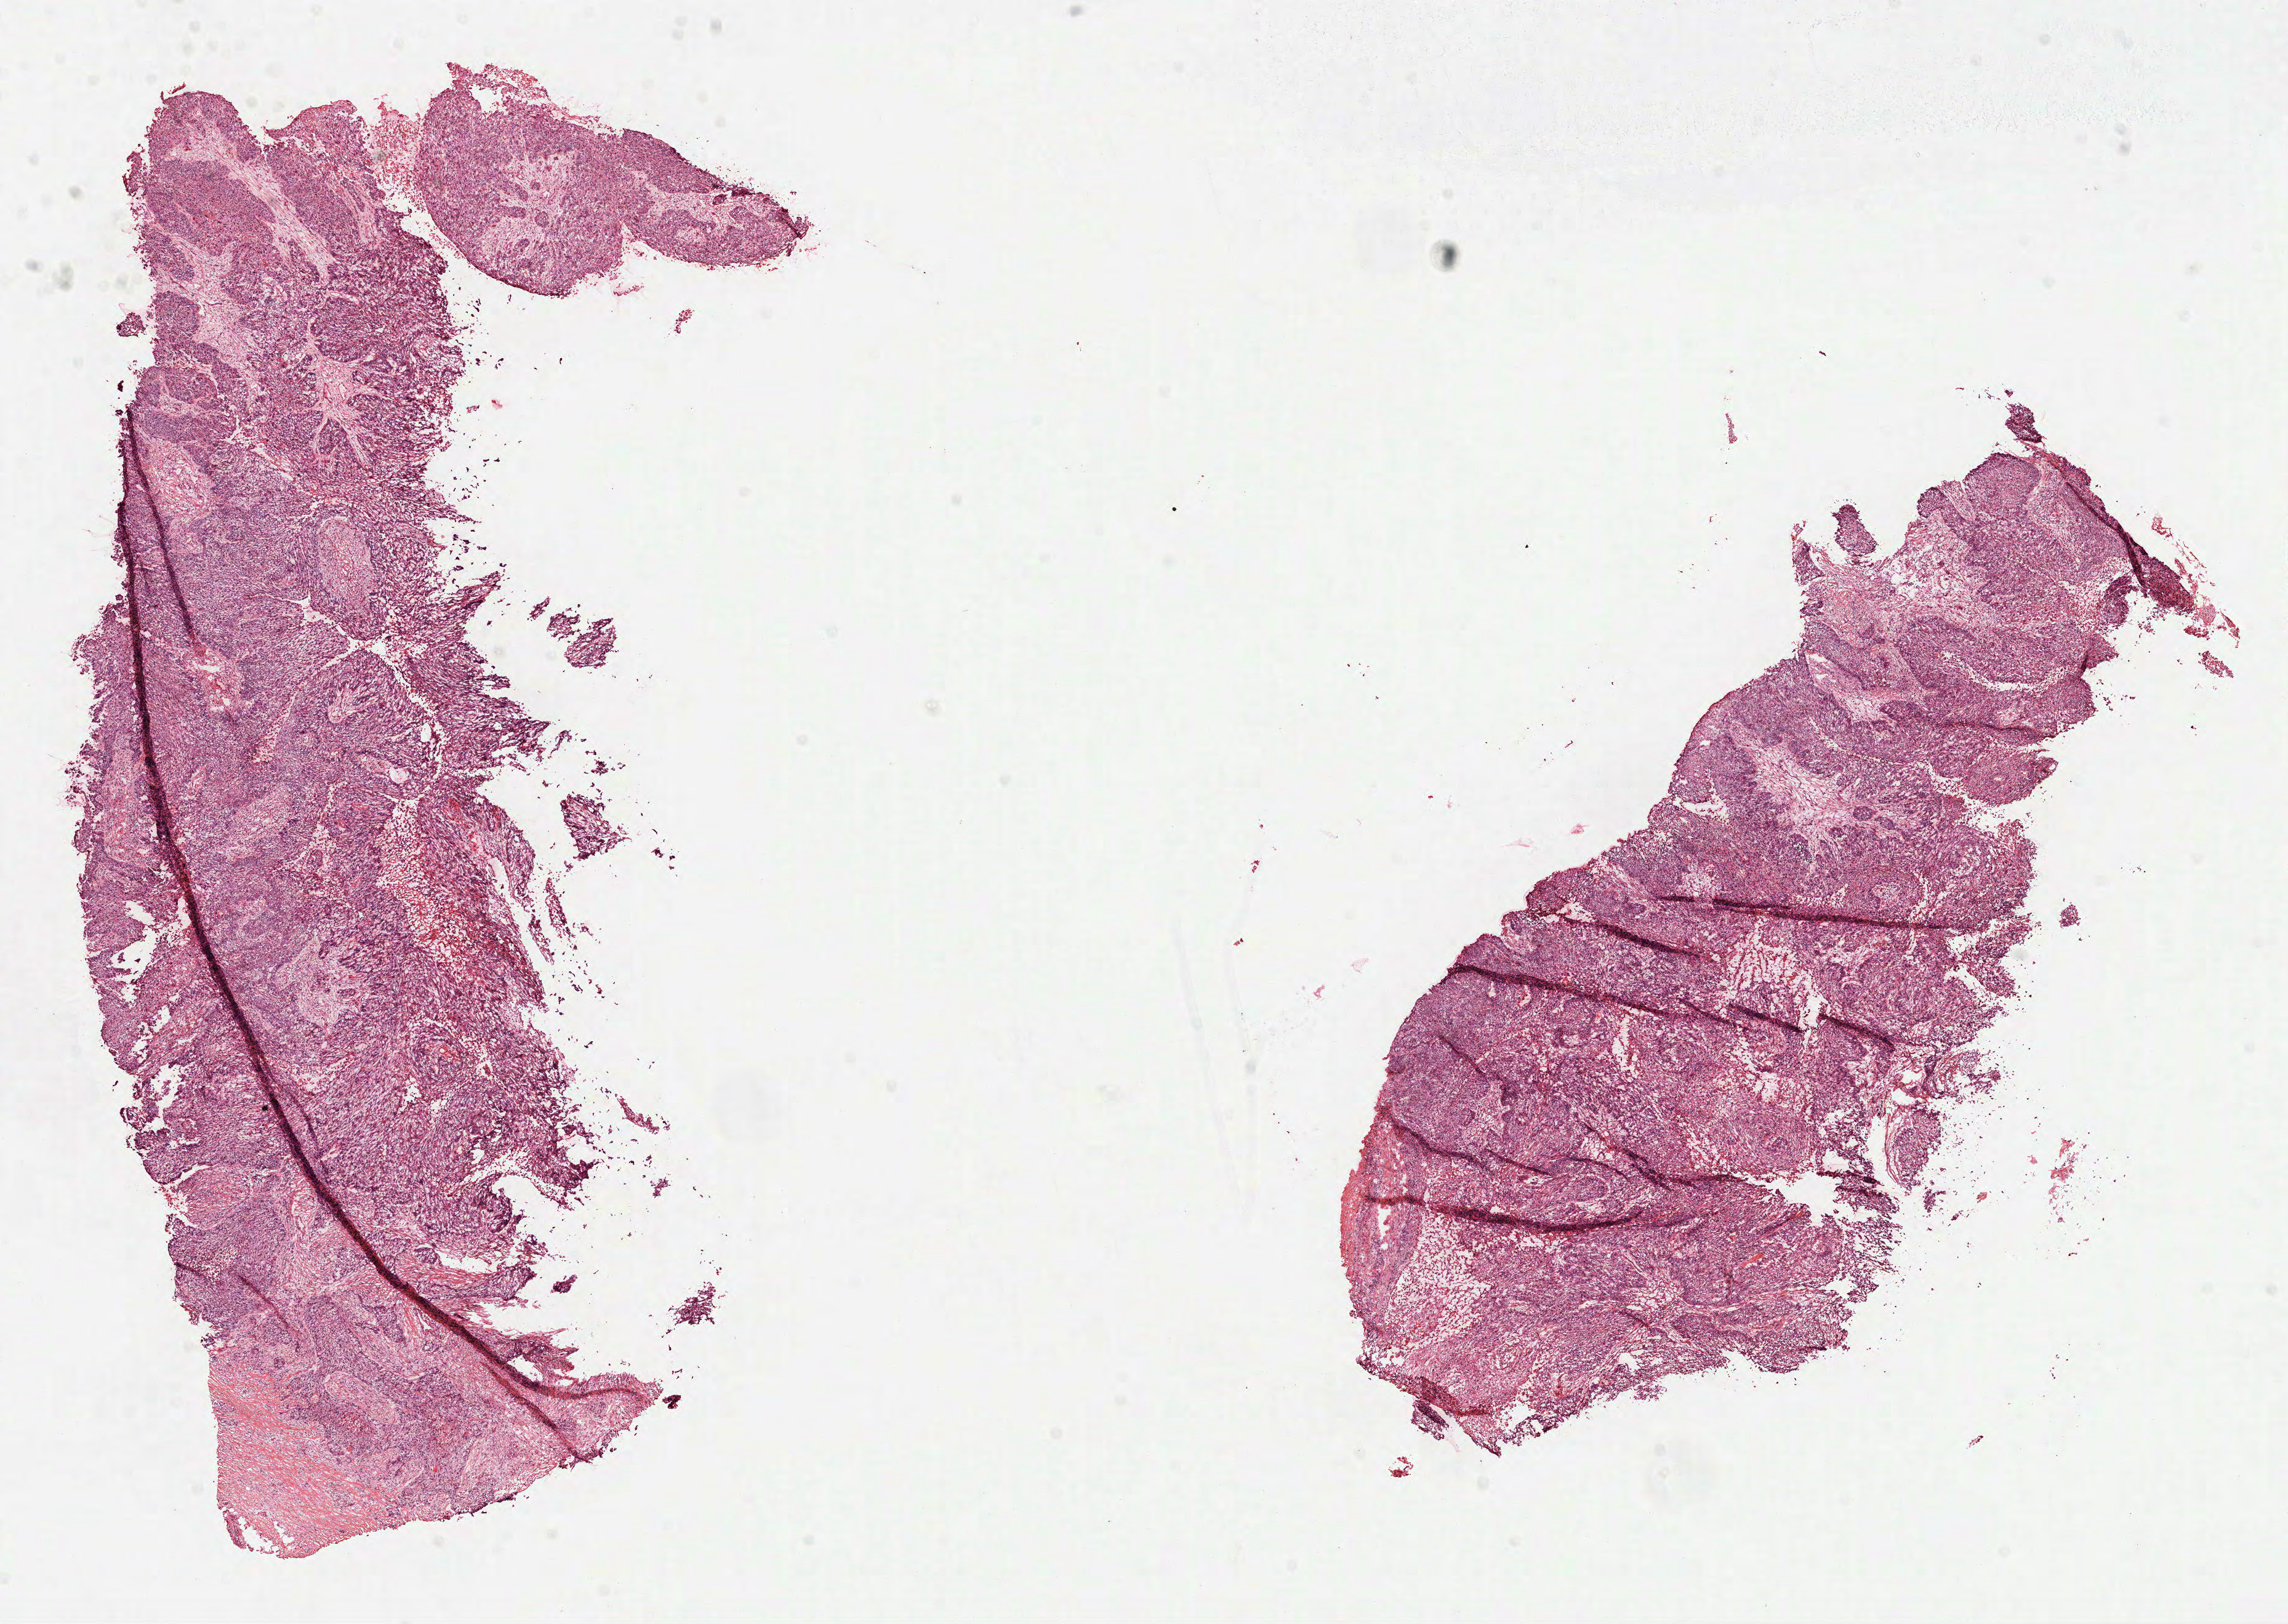
H&E whole-slide image, a low-resolution overview of the entire scanned area, about 15.0 x 10.6 mm; formalin-fixed paraffin-embedded (FFPE) diagnostic section; primary tumour sample from the lung. Patient: male, age at initial diagnosis 75 years.
AJCC pathologic stage: IB. TNM: T2 N0 M0. Pathologic diagnosis: Squamous cell carcinoma, NOS.